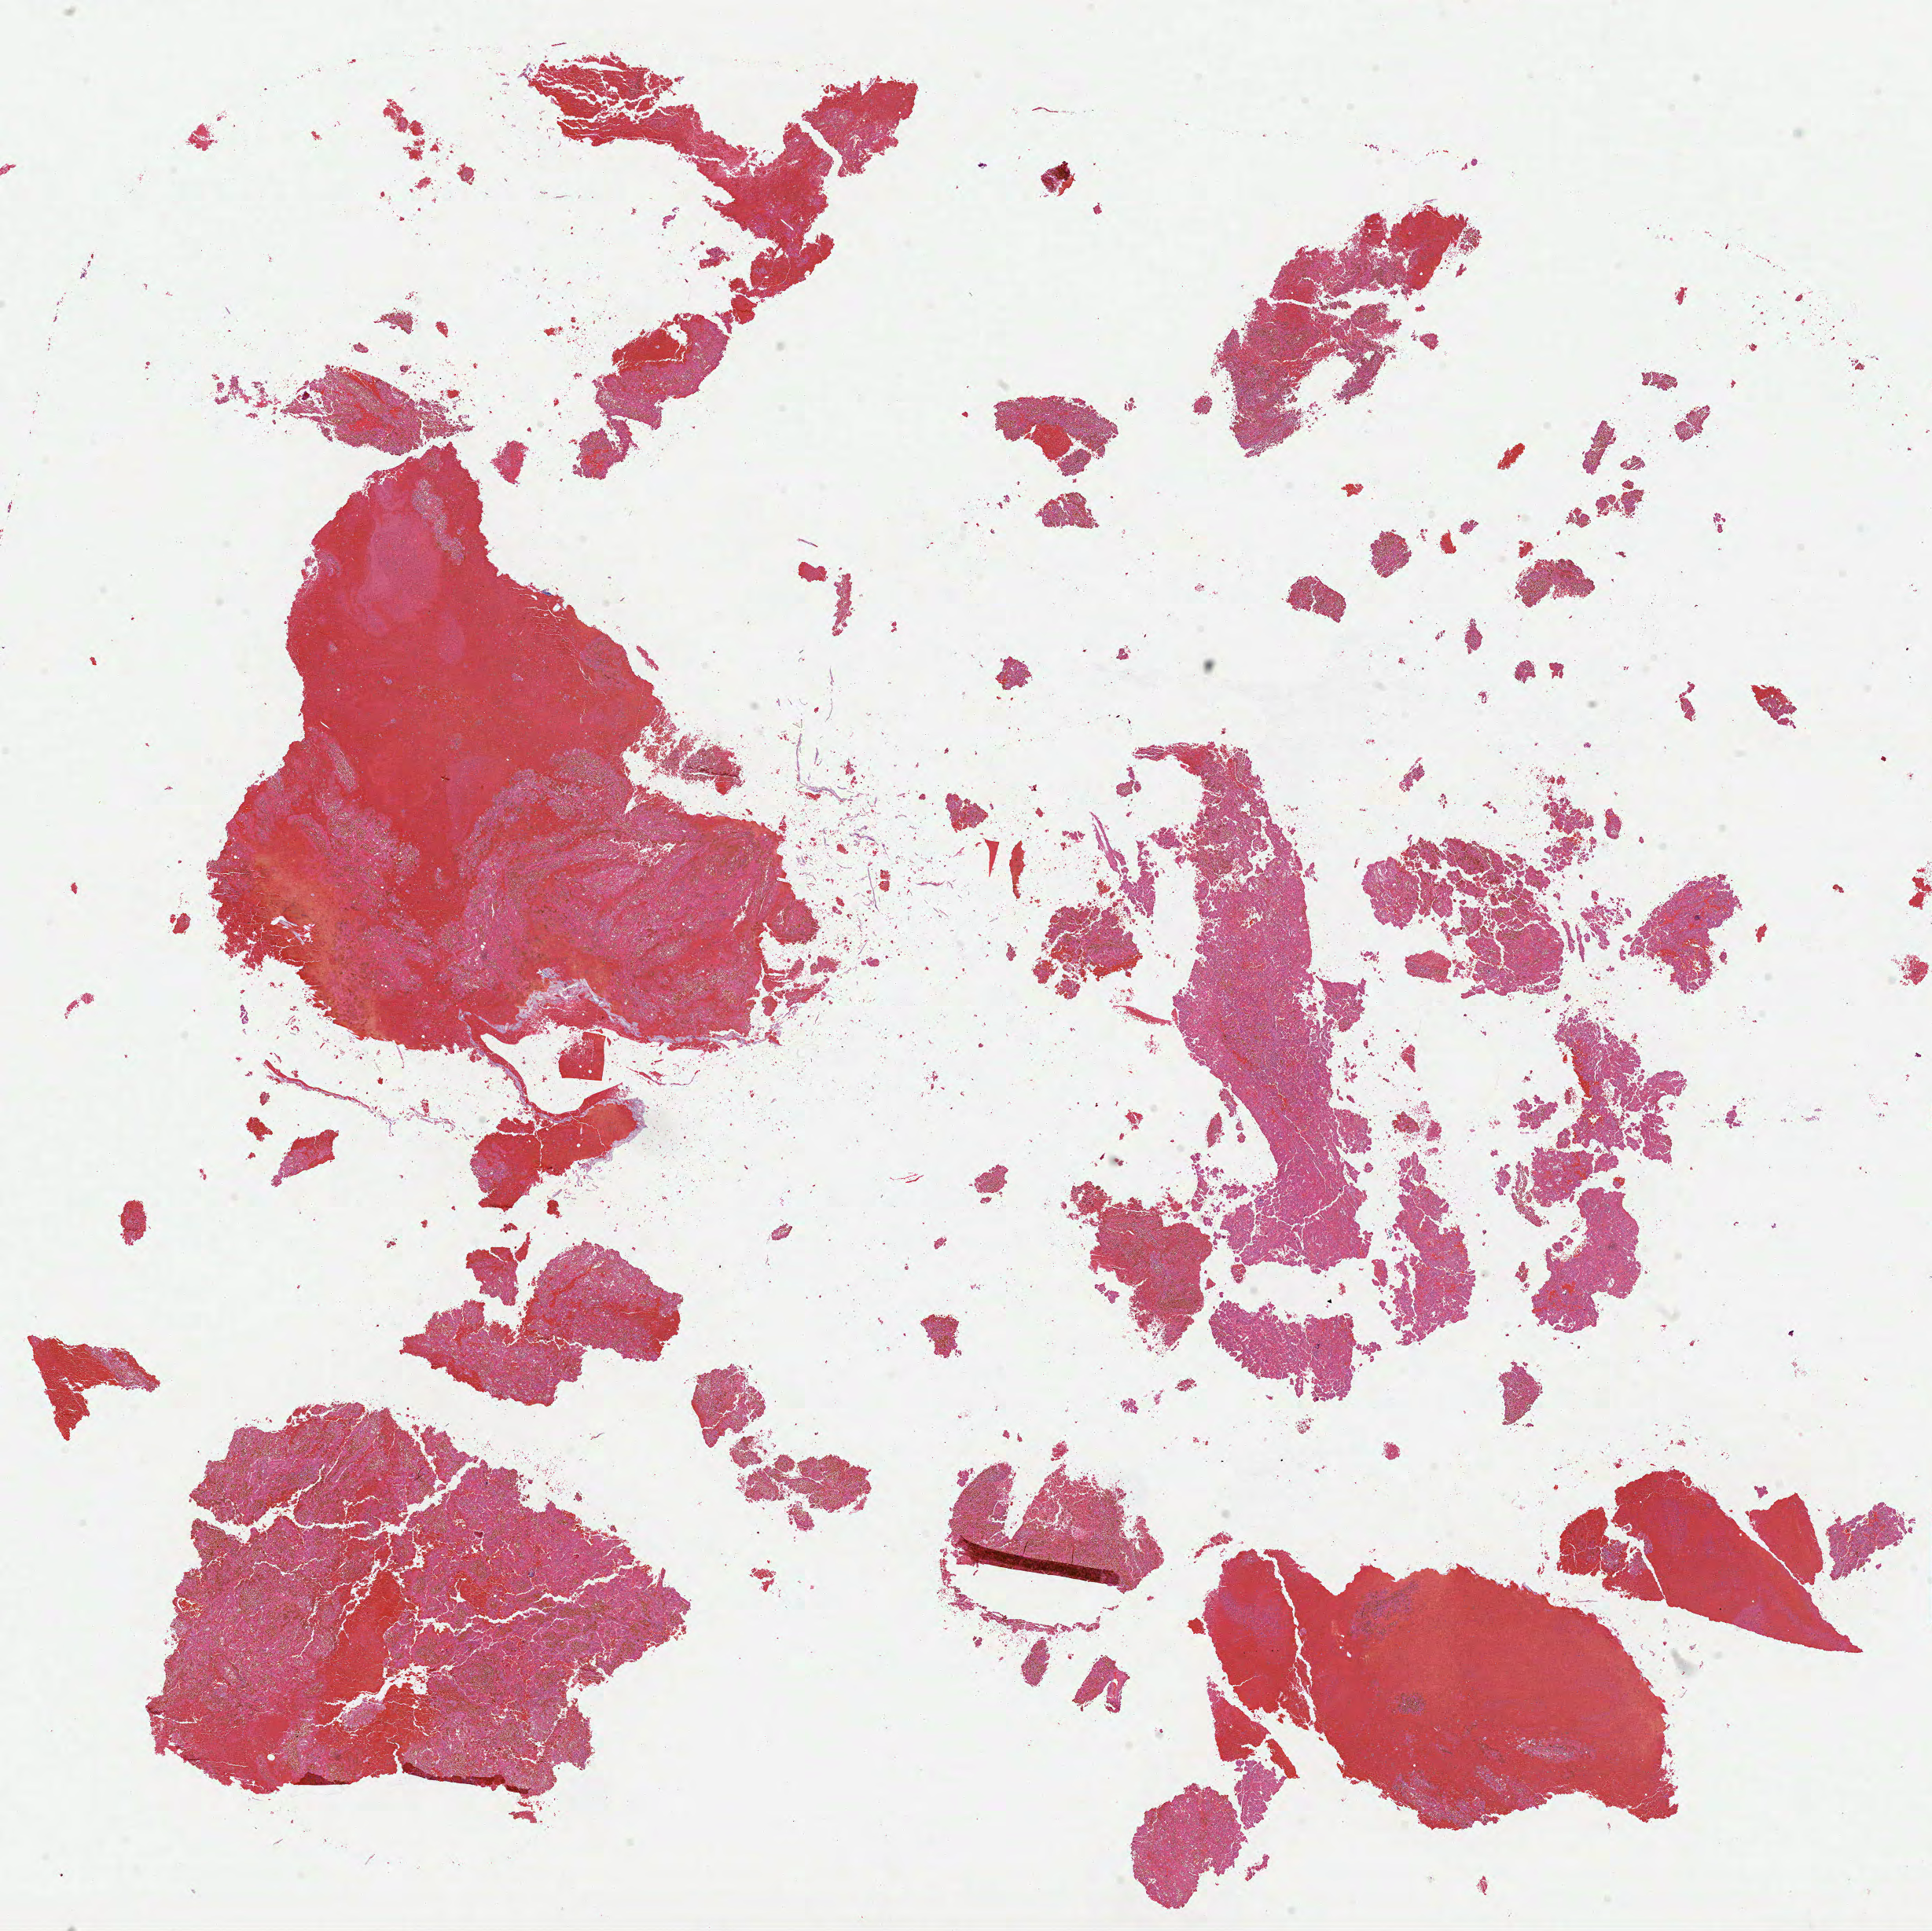
Whole-slide histology image, H&E — shown as a low-resolution overview of the whole scanned area (about 19.8 x 19.8 mm, from a 40x scan); FFPE section; sample: primary tumour, kidney. Patient: male, age at initial diagnosis 84 years.
Histologic diagnosis: Papillary adenocarcinoma, NOS. AJCC pathologic stage: I (7th edition).